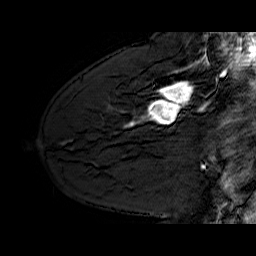
Breast MRI (dynamic contrast-enhanced), one sagittal slice; slice 42 of 60 in the series (ordered by position); dynamic contrast-enhanced series, time point 2 of 6 at this slice position (early post-contrast); 1.5 T; TE 6.4 ms, TR 32.9 ms; 4 mm slice thickness; 256 × 256 image matrix, field of view 200 × 200 mm. Female patient. Case-level facts recorded for this patient, not image findings: setting: breast cancer imaged before/during neoadjuvant chemotherapy; receptor status: HER2-positive.
Annotated regions visible in this slice (semi-automatically segmented with operator editing):
- analysis volume of interest (the breast-tissue region the enhancement analysis was run in; not a lesion): bounding box [x1, y1, x2, y2] px = [130, 62, 210, 128]
- tumour enhancement mask (voxels above the 100 % enhancement threshold inside the analysis volume of interest): [130, 62, 200, 126]